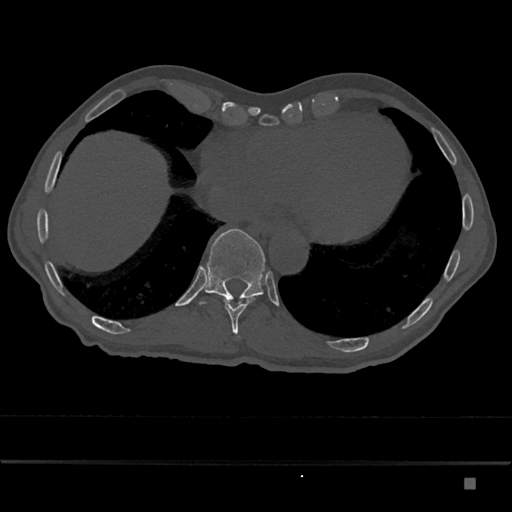
CT including the spine, one axial slice. Position 710 of 797 along the scan axis. Reconstruction kernel Br40s/3. 120 kVp. Bone window (W 1800 / L 400 HU). 512 × 512 image matrix, field of view 390 × 390 mm. Male patient, age 72 years. Case-level facts recorded for this patient, not image findings: primary cancer: prostate.
Structures marked on this image (semi-automatic segmentation, software-assisted and operator-edited):
- T10 vertebra: box from (x=224, y=296) to (x=254, y=337) px
- T11 vertebra: (x=199, y=229)–(x=266, y=305)